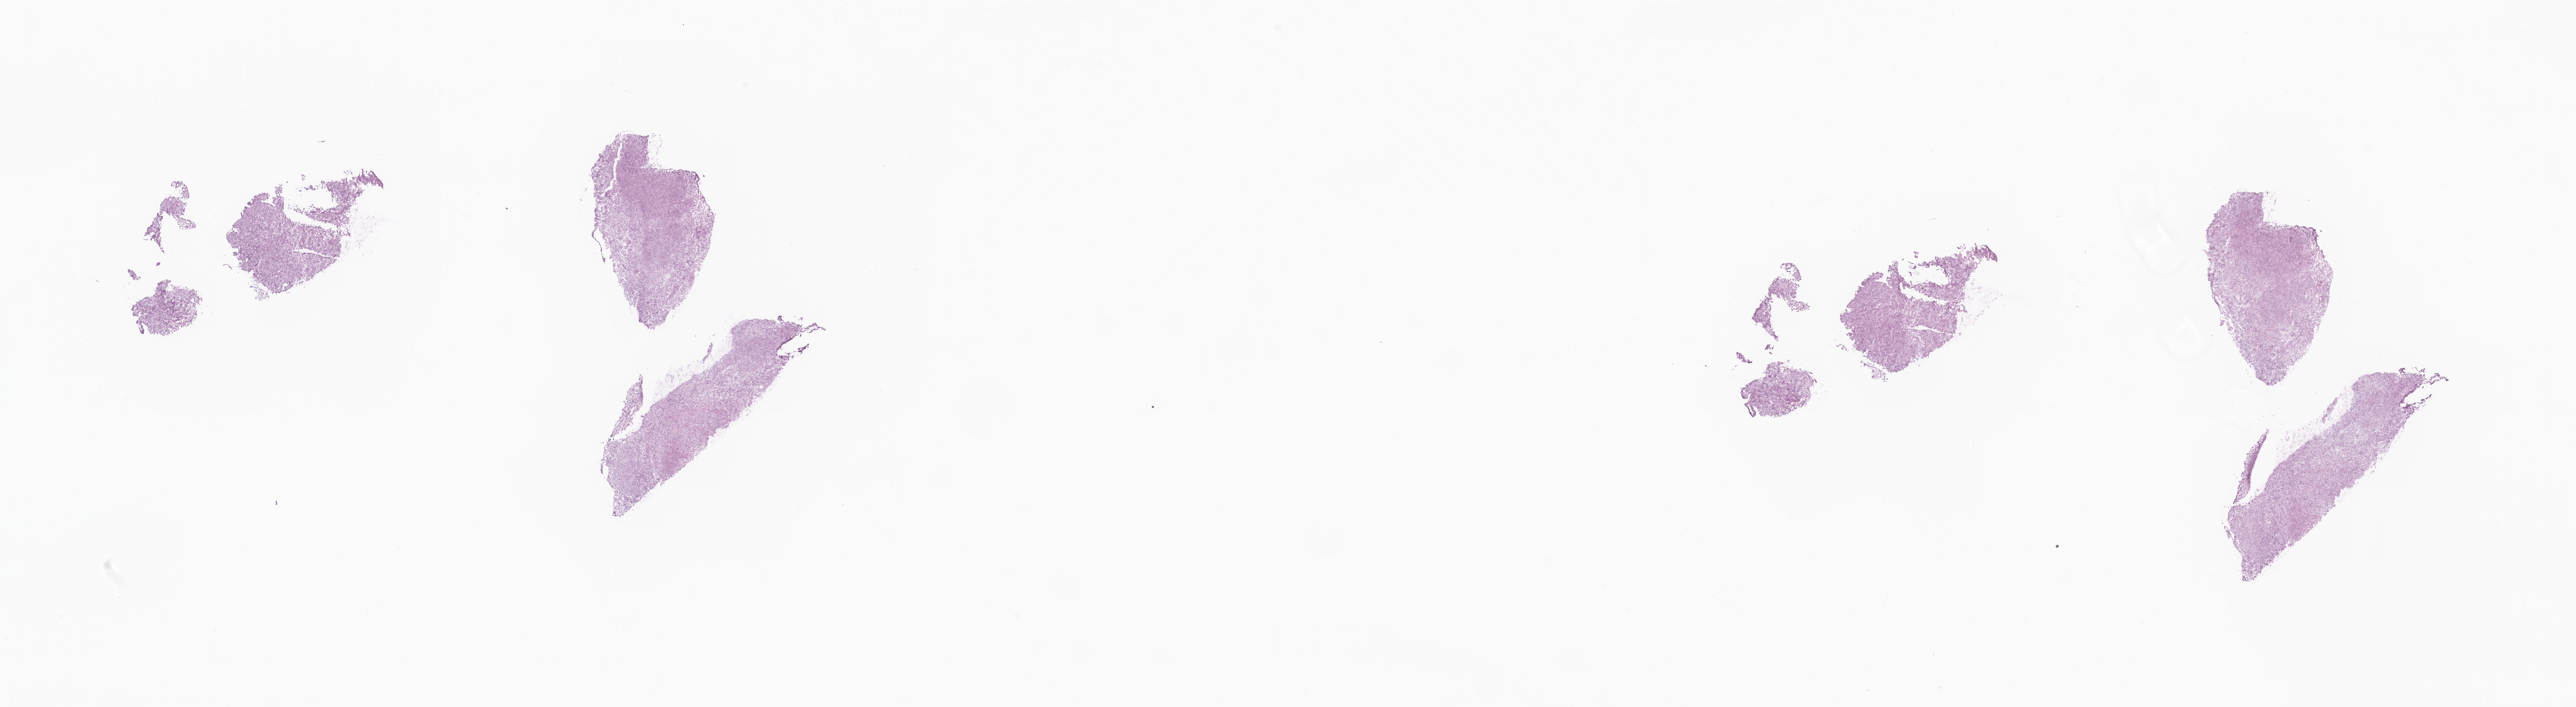
Digitized hematoxylin and eosin (H&E)-stained section — whole scanned area (about 36.9 x 10.1 mm) shown as a low-resolution overview, cryosection, specimen: primary tumor, site: pancreas. Female, age 76 years at initial diagnosis. Slide review estimates, as recorded: tumor cells 90%, tumor nuclei 95%, stromal cells 10%, necrosis 0%, normal cells 0%. Infiltration values recorded for this section: lymphocyte infiltration 0%, monocyte infiltration 0%, neutrophil infiltration 0%.
* section: bottom of the tissue portion
* histologic diagnosis: Leiomyosarcoma, NOS